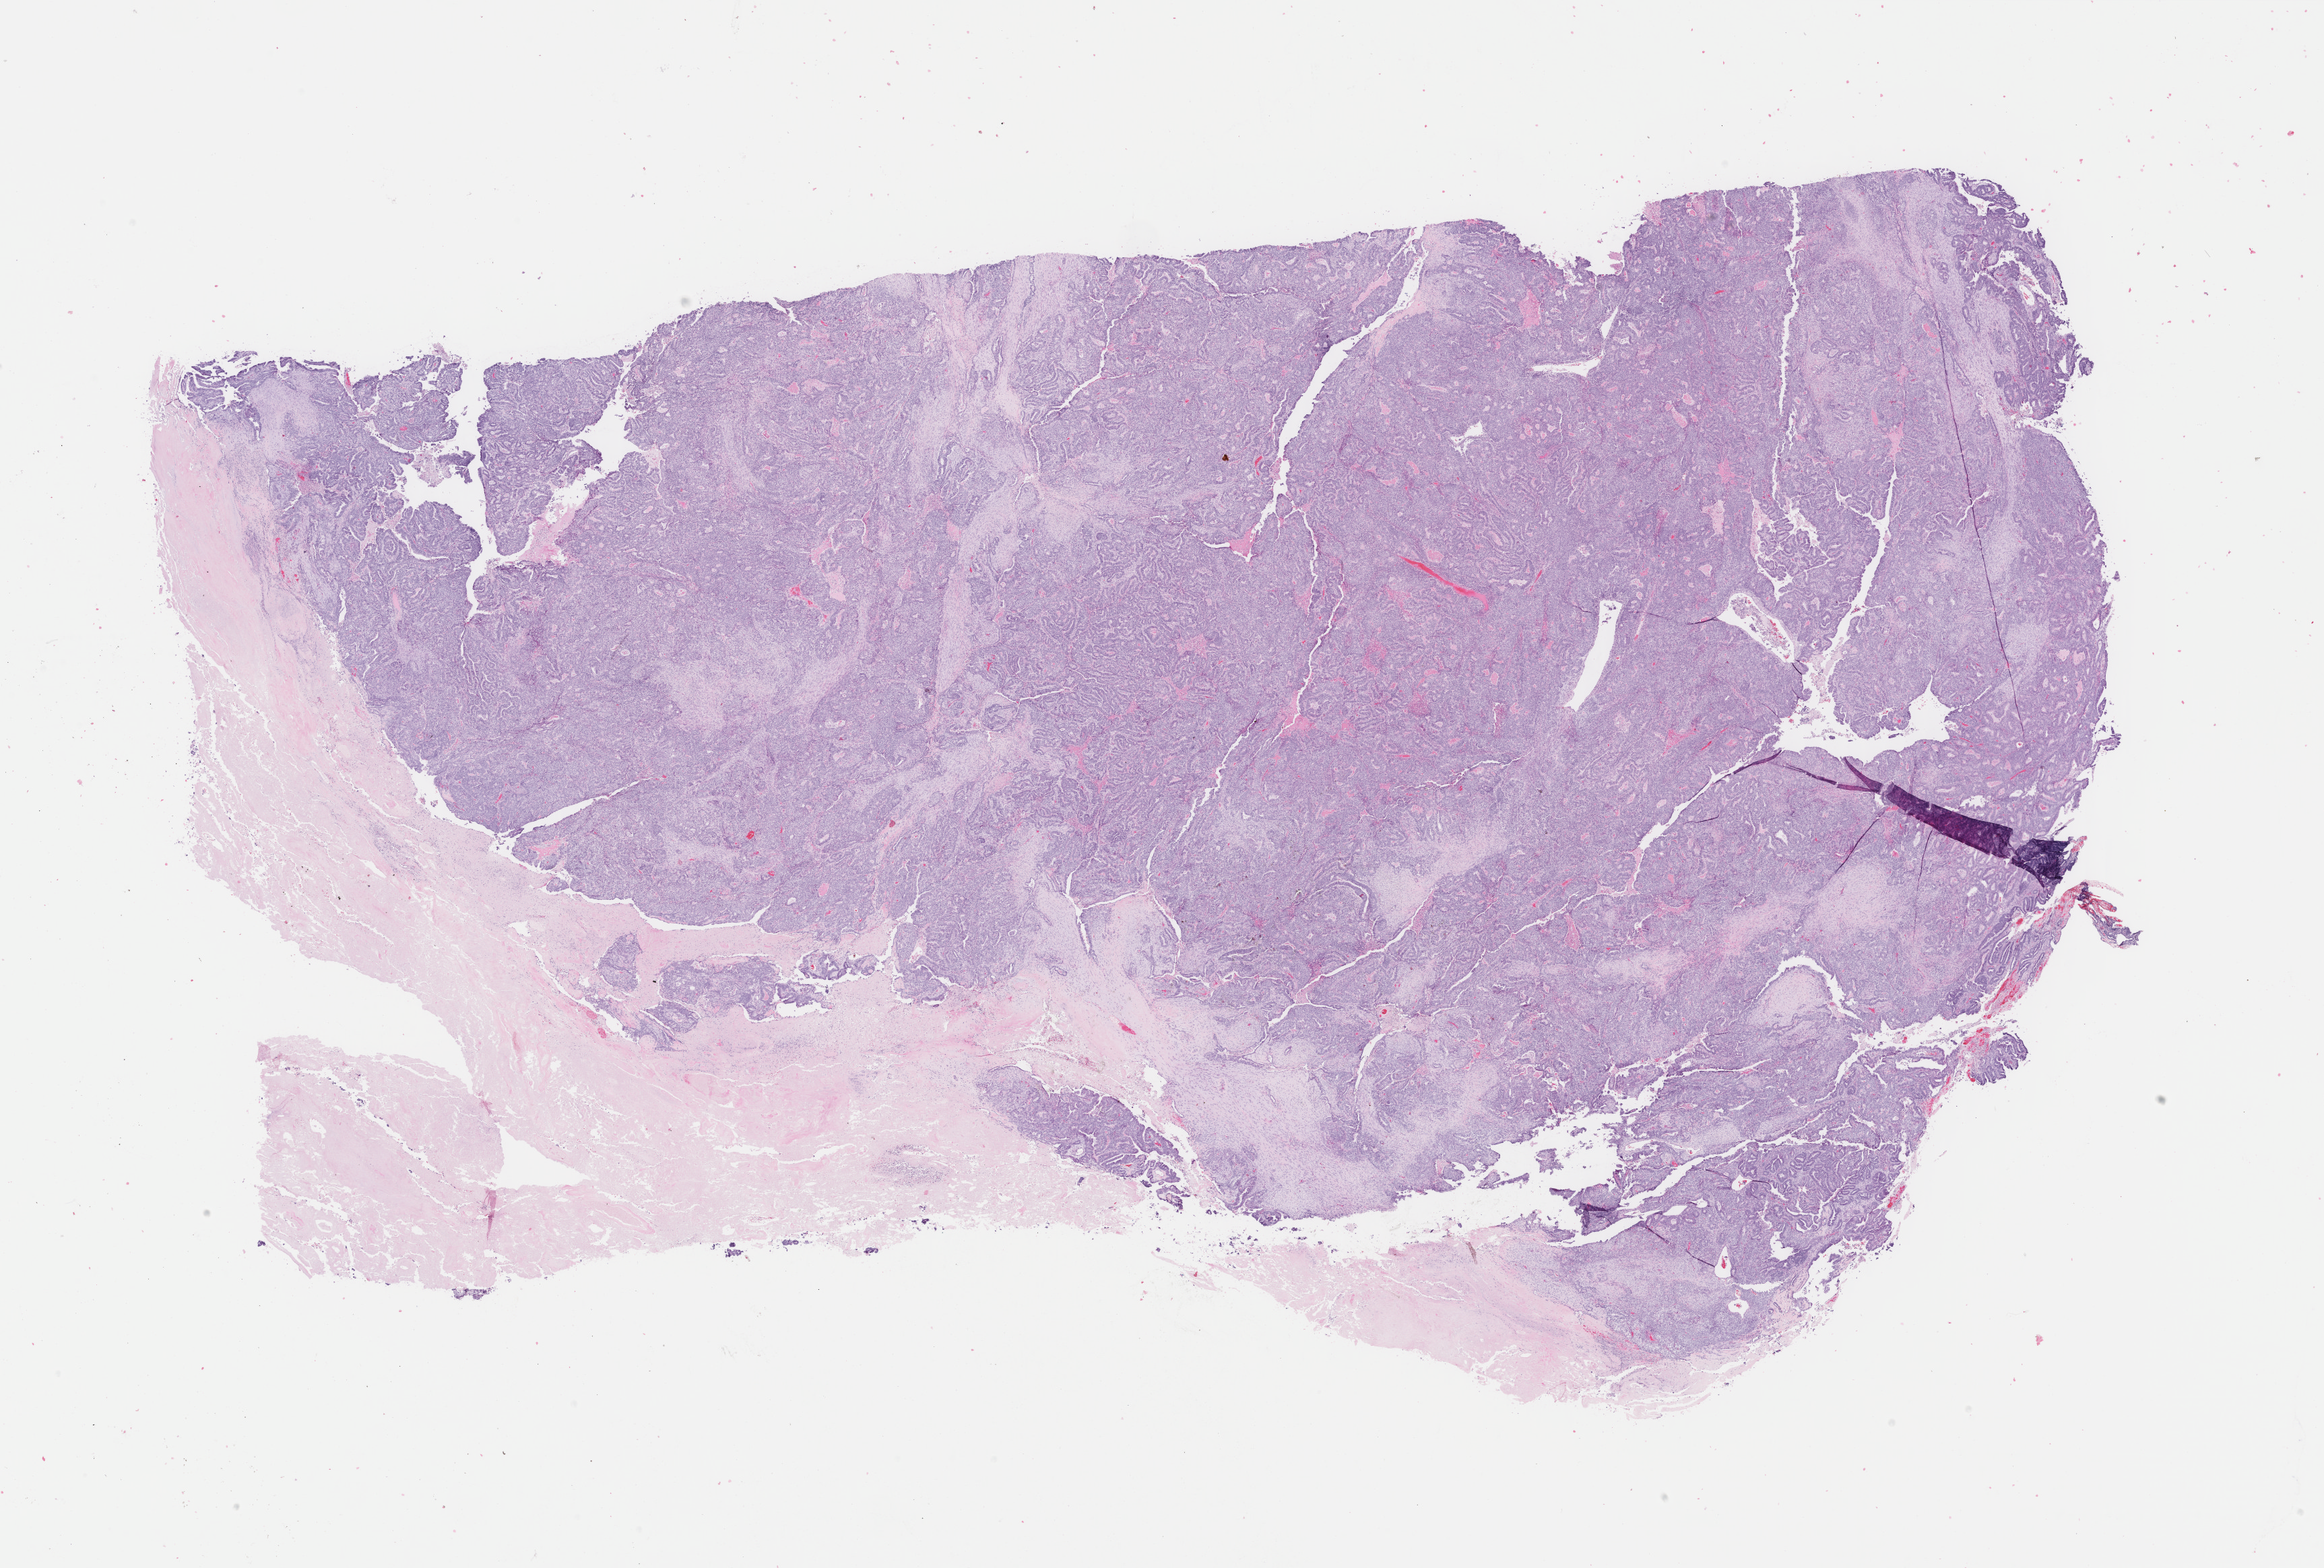
Whole-slide histology image, Hematoxylin and eosin (H&E) stained — low-resolution overview of the scanned area, about 27.4 x 18.5 mm (acquisition: 40x scan), formalin-fixed paraffin-embedded (FFPE) diagnostic section, sample: primary tumour, uterus. Female patient; age at initial diagnosis 60 years. Histologic grade: G3 (poorly differentiated).
Lymph nodes positive (case pathology): 1 of 19 examined. FIGO stage: IIIC1. Diagnosis: Endometrioid adenocarcinoma, NOS.